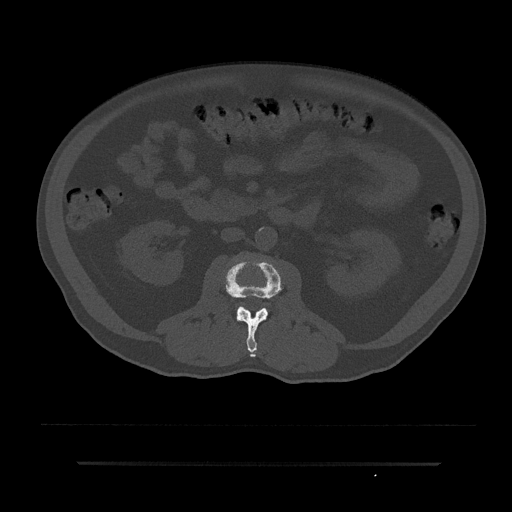
CT including the spine, one axial slice; position 52 of 797 along the scan axis; reconstruction kernel Br40s/3; 120 kVp; bone window (W 1800 / L 400 HU); 0.5 mm slice thickness; 512 × 512 image matrix, field of view 464 × 464 mm. Male patient, age 59 years. From the clinical record (not read from this slice): primary cancer: bile ducts.
Outlined on this slice (semi-automatic segmentation, software-assisted and operator-edited):
- L2 vertebra: bounding box <223,260,284,357> (left, top, right, bottom; pixels)